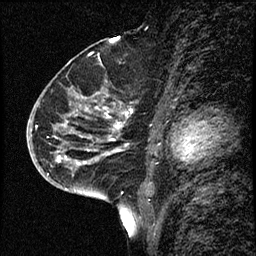
Breast MRI (dynamic contrast-enhanced), one sagittal slice; slice 37 of 68 in the series (ordered by position); dynamic contrast-enhanced study with each time point stored as its own series, time point 2 of 3 at this slice position (early post-contrast, ordered by acquisition time); 1.5 T; TE 4.2 ms, TR 17.6 ms; 2 mm slice thickness; 256 × 256 image matrix, field of view 200 × 200 mm. Patient: female, 52 years. From the clinical record (not read from this slice): setting: breast cancer imaged before/during neoadjuvant chemotherapy; receptor status: HER2-positive.
Outlined on this slice (semi-automatic segmentation, software-assisted and operator-edited):
- analysis volume of interest (the breast-tissue region the enhancement analysis was run in; not a lesion): bounding box (x1, y1, x2, y2) in pixels: (50, 61, 131, 184)
- tumour enhancement mask (voxels above the 100 % enhancement threshold inside the analysis volume of interest): (57, 113, 127, 165)